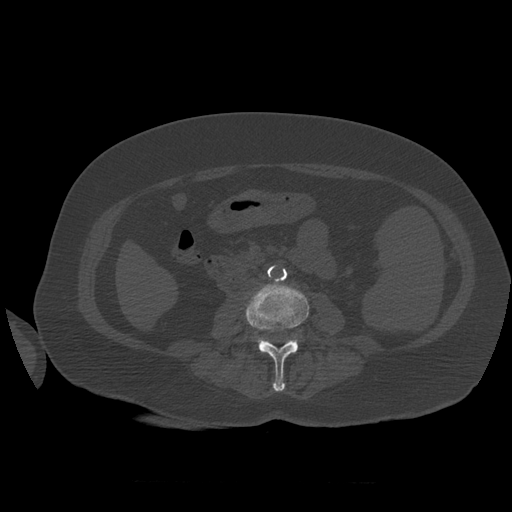
CT including the spine, one axial slice; slice 224 of 399 in the series (ordered by position); bone window (W 1800 / L 400 HU); 1.25 mm slice thickness; 512 × 512 image matrix, field of view 404 × 404 mm. Patient age 81 years. From the clinical record (not read from this slice): primary cancer: renal; vertebrae with lytic lesions (as recorded): L1.
Structures marked on this image (semi-automatic segmentation, software-assisted and operator-edited):
- L3 vertebra: bounding box [x1, y1, x2, y2] px = [246, 282, 310, 392]